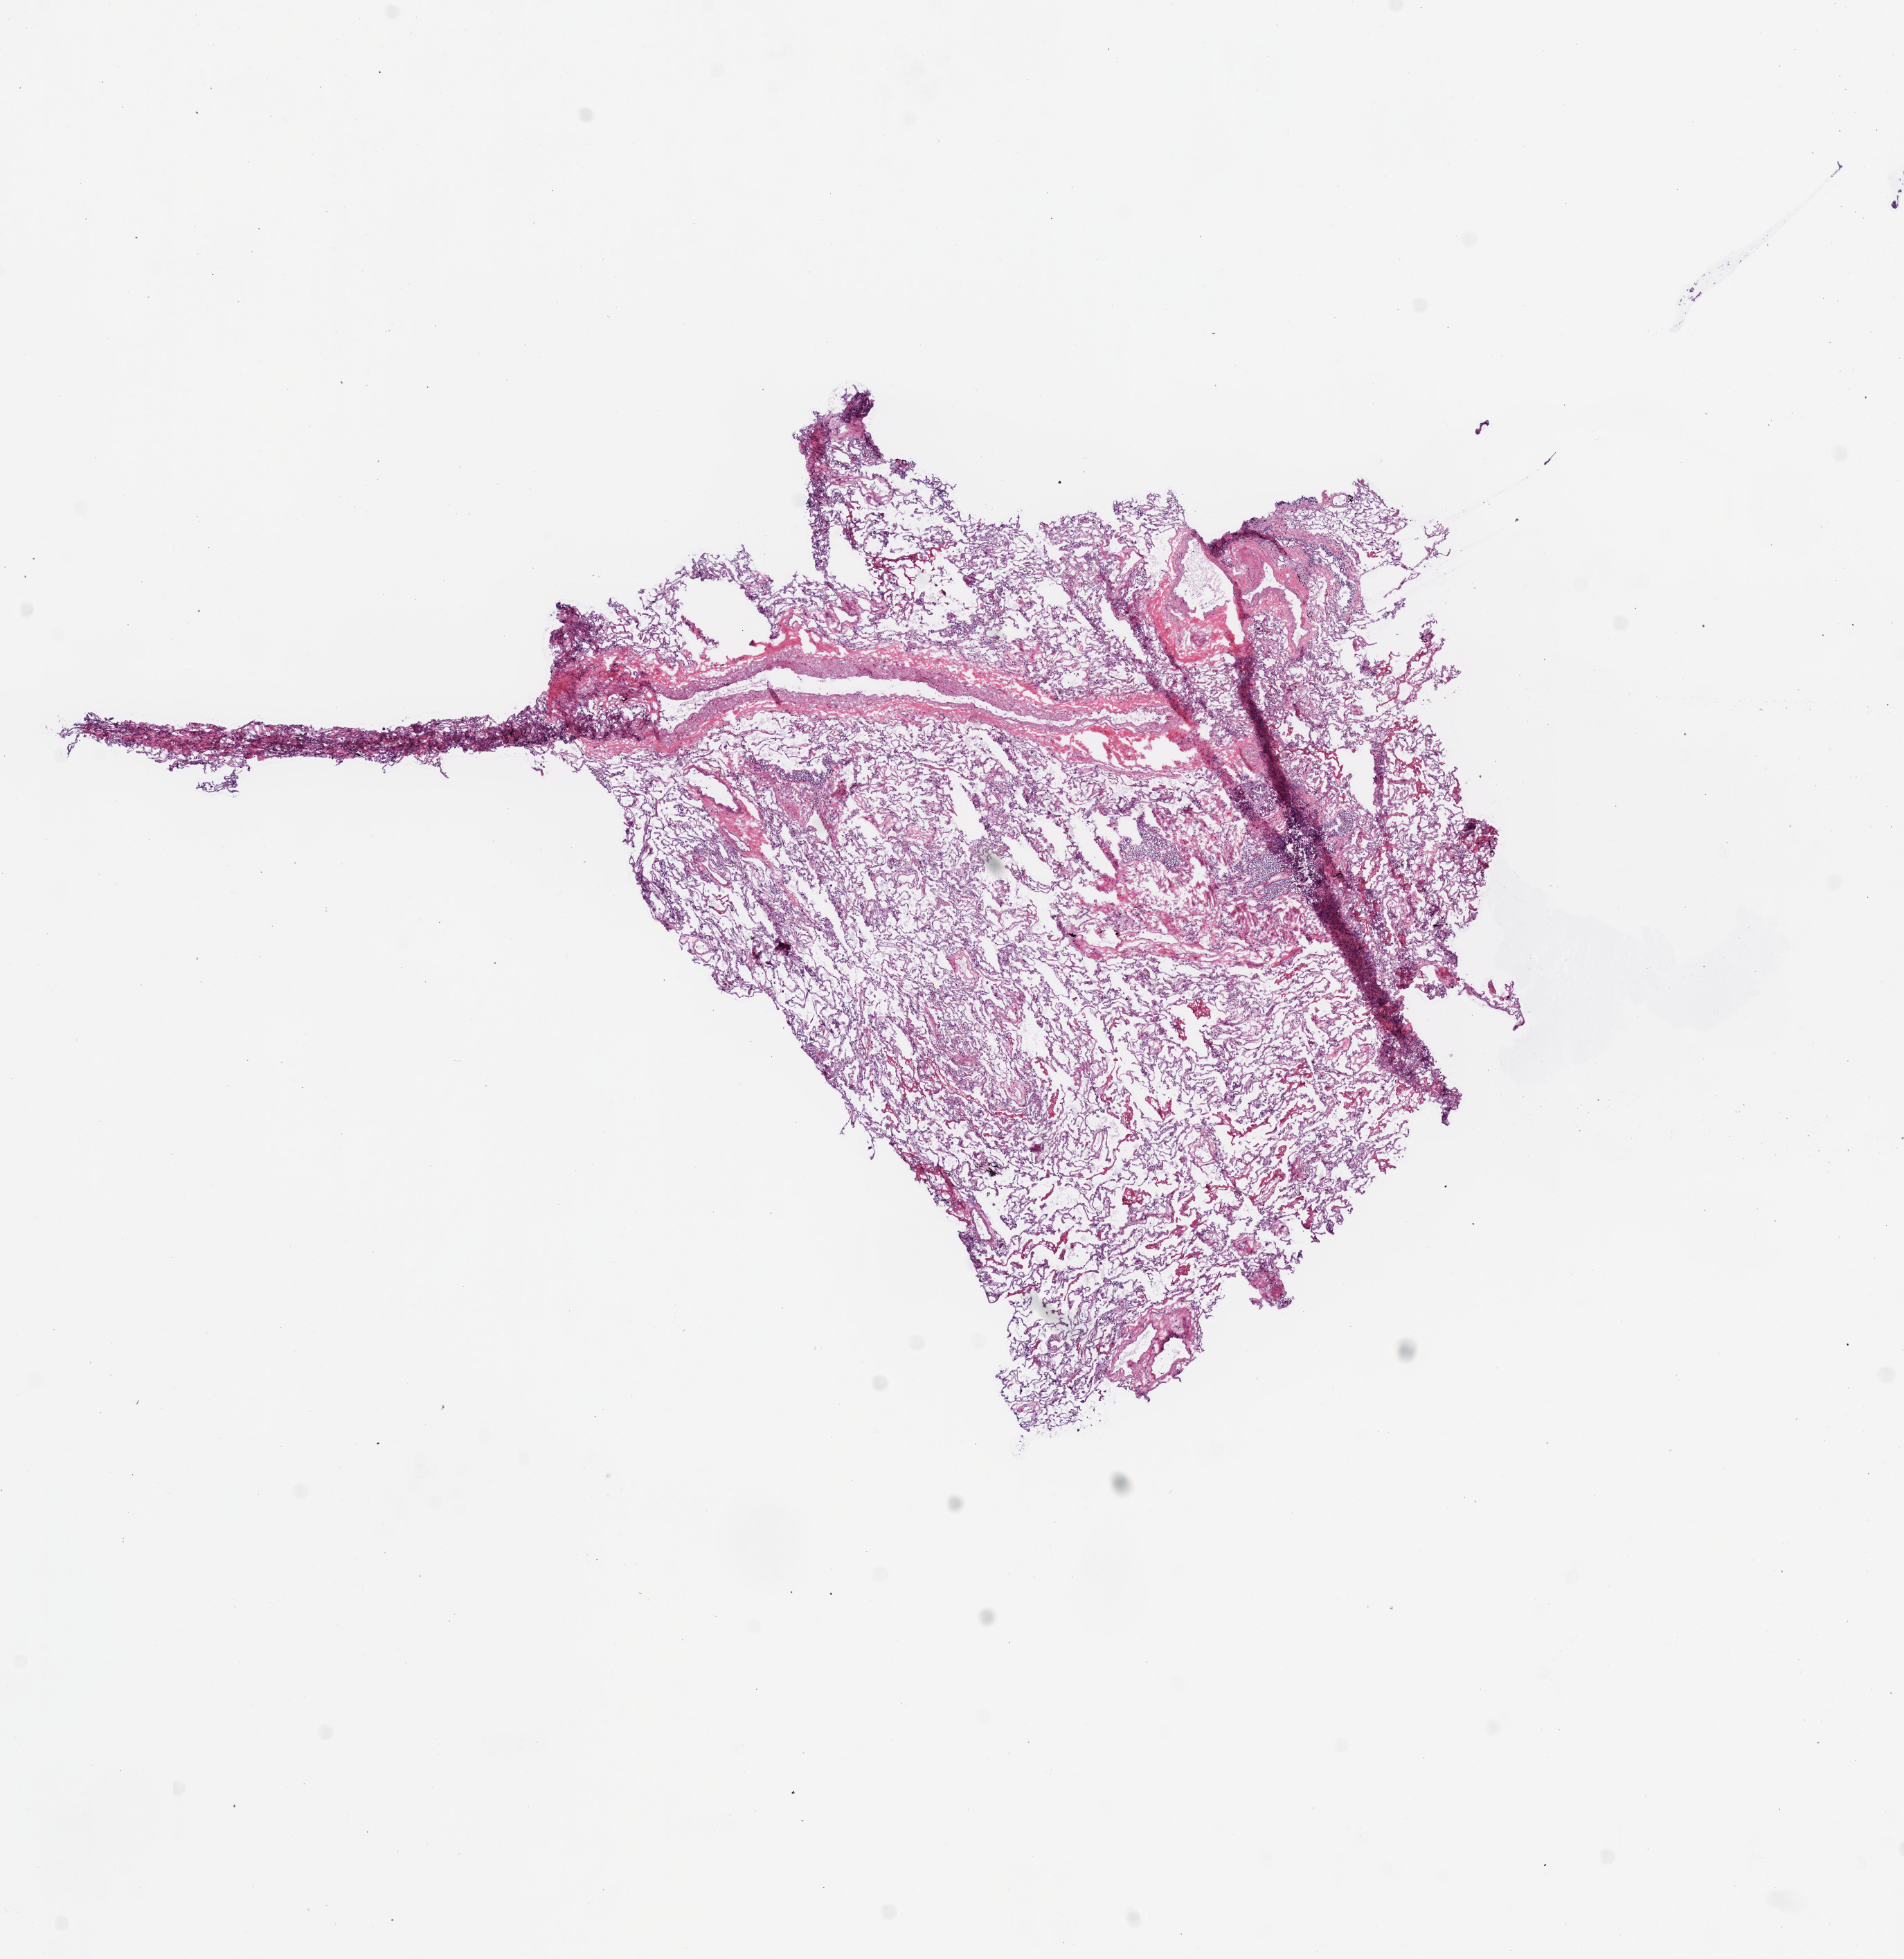
H&E-stained whole-slide image, a low-resolution overview of the entire scanned area, about 11.0 x 11.4 mm (acquisition: 20x scan); frozen section; solid tissue normal (non-tumour tissue) sample from the lung. Patient: male, age at initial diagnosis 81 years.
This section: solid tissue normal sample (biorepository sample class). Patient diagnosis: Squamous cell carcinoma, NOS (lower lobe, lung).